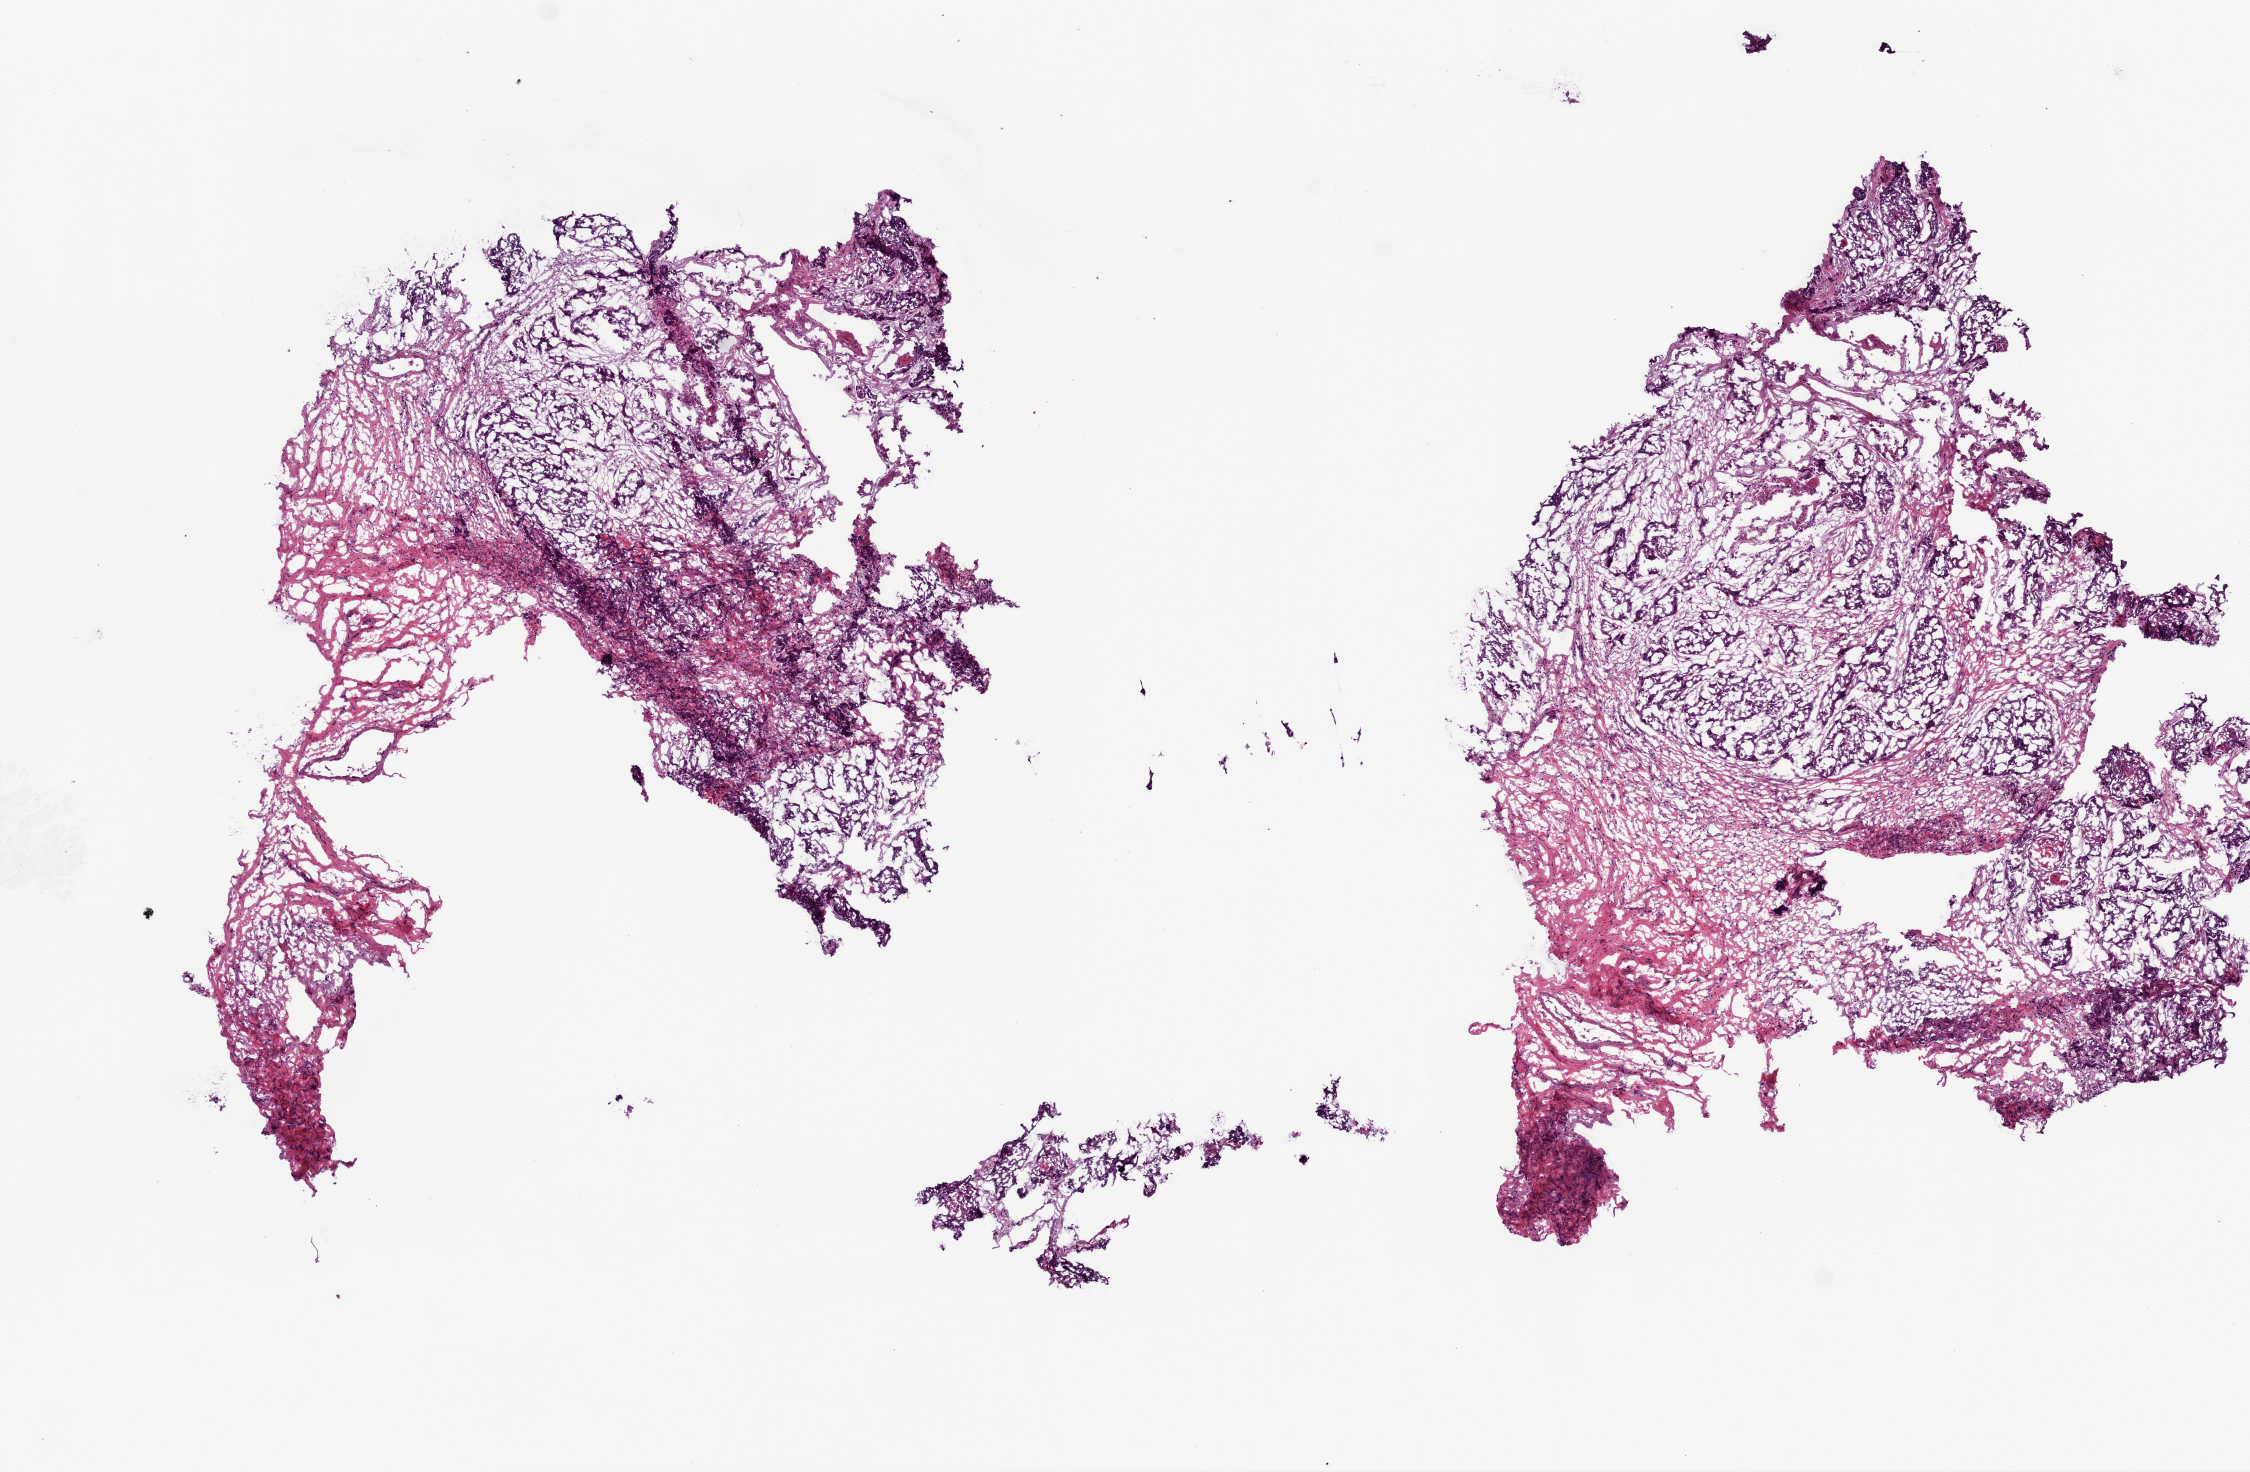
Digitized H&E-stained tissue section (whole slide), shown as a low-resolution overview of the whole scanned area (about 9.0 x 5.9 mm, slide scanned at 20x). Frozen section. Primary tumour sample from the head and neck. Male, age 52 years at initial diagnosis. Histologic grade: G3 (poorly differentiated). Pathologist review of this section (percent, as recorded): tumour cells 60%, tumour nuclei 70%, normal cells 0%, stromal cells 40%, necrosis 0%.
- lymph nodes positive (case pathology): 42 of 47 examined
- AJCC pathologic stage: IVA (7th edition)
- histologic diagnosis: Squamous cell carcinoma, NOS